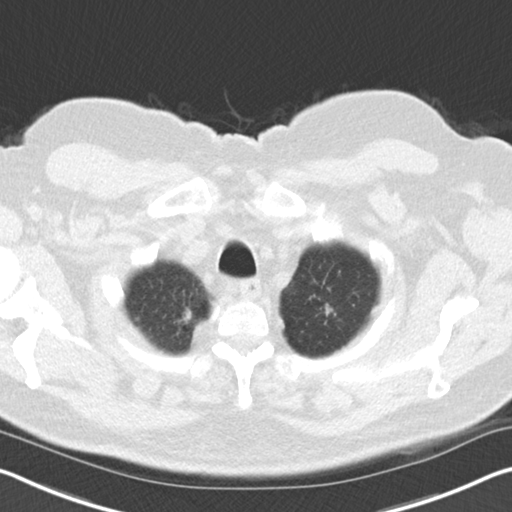
Axial slice from a low-dose chest CT screening exam, second annual screen, lung window (W 1500 / L -600 HU), standard (soft-tissue) reconstruction kernel (B30f), 120 kVp. Male, age 67 years at enrolment. Former smoker at enrolment.
• Expert reader's lesion annotation, box from (x=305, y=295) to (x=345, y=334) px.
• No non-calcified nodule or mass ≥4 mm was recorded by the screening reader at this exam.
• Official screen result: negative screen, minor abnormalities not suspicious for lung cancer.
• Participant outcome: lung cancer diagnosed 507 days after this screen (after the third annual screen) — adenocarcinoma, NOS, left upper lobe, moderately differentiated (G2), stage IIA (AJCC 6th edition), 18 mm at pathology.